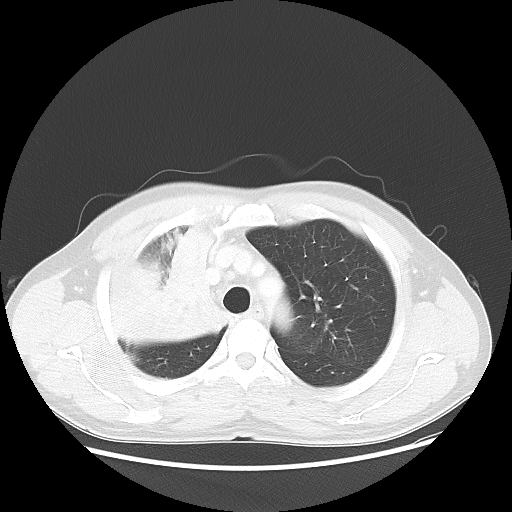
Chest CT, one axial slice. Slice 42 of 56 in the series (ordered by position). Lung window (W 1500 / L -600 HU). 5 mm slice thickness. 512 × 512 image matrix. Patient: male, 60 years. Case-level facts recorded for this patient, not image findings: clinical TNM (as recorded): T2a N1 M0.
Structures marked on this image (bounding box drawn by a radiologist):
- lung tumour (recorded histology: squamous cell carcinoma): bounding box <108,220,247,362> (left, top, right, bottom; pixels)